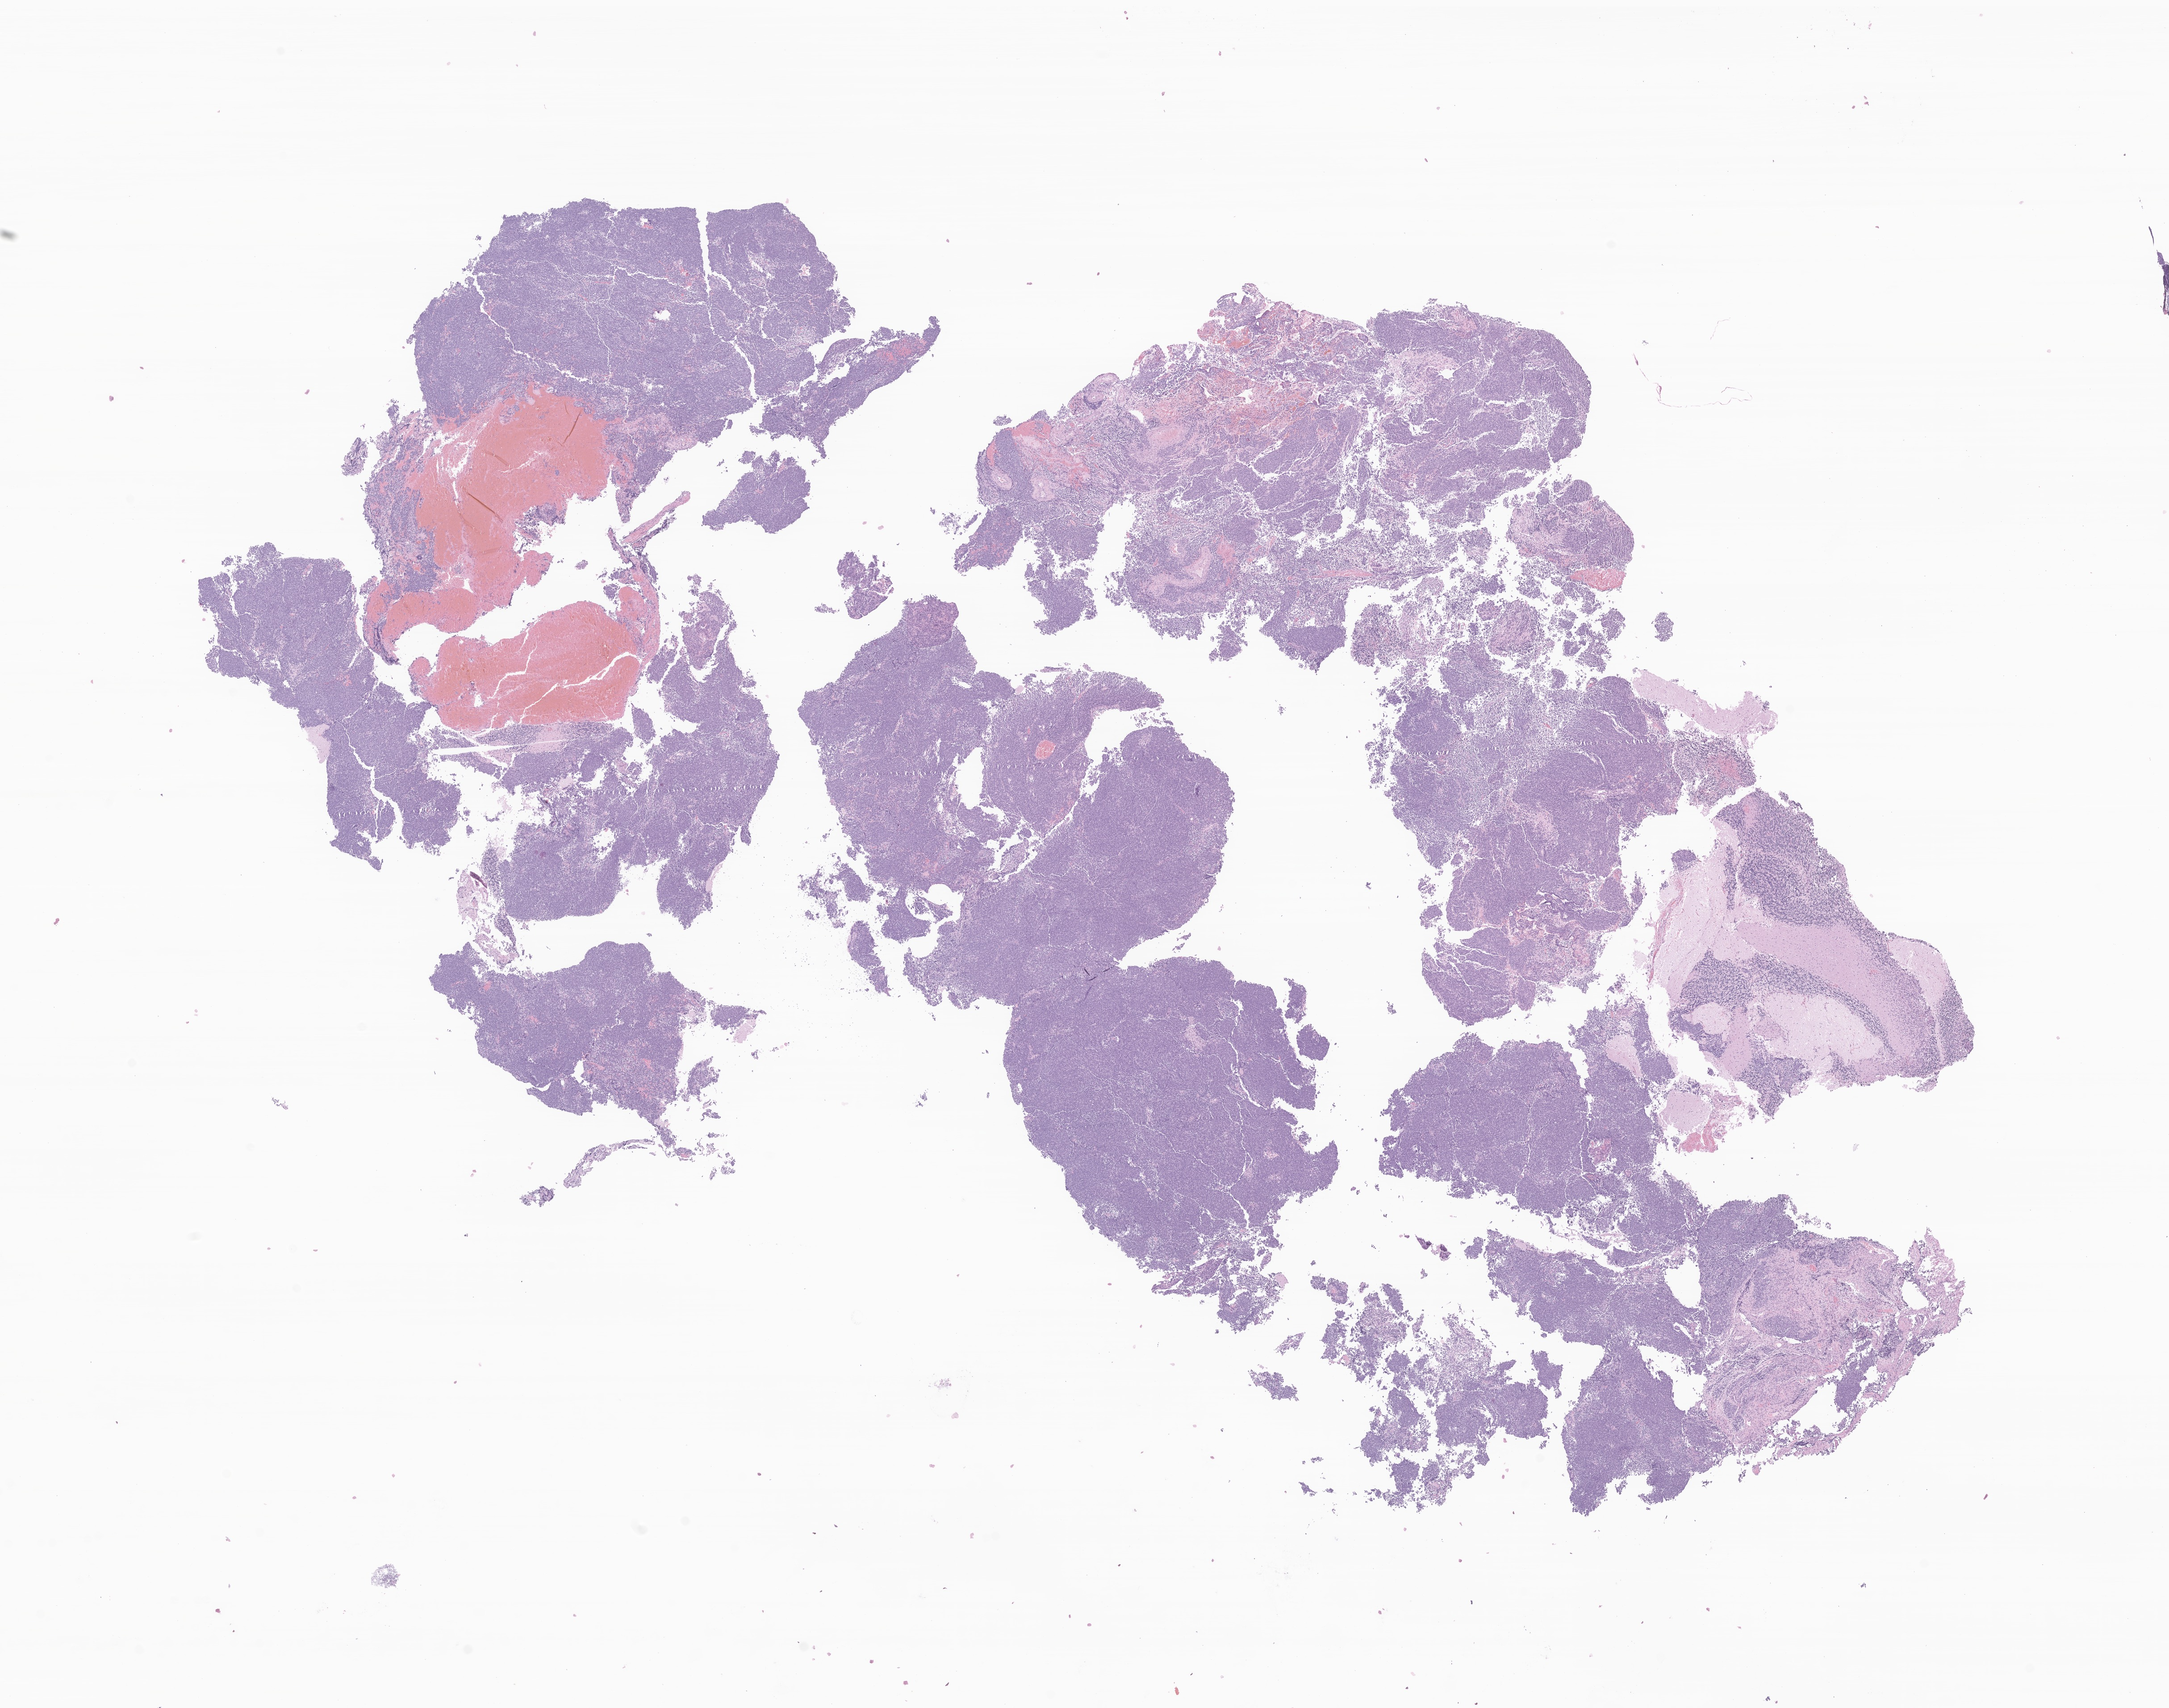
Whole-slide image, H&E stain of tumor tissue from the brain, low-resolution overview of the scanned area, about 20.5 x 16.1 mm. Formalin-fixed paraffin-embedded section. Patient female; age 75 months (6 years 3 months).
* diagnosis (ICD-O-3 morphology term): Medulloblastoma, NOS